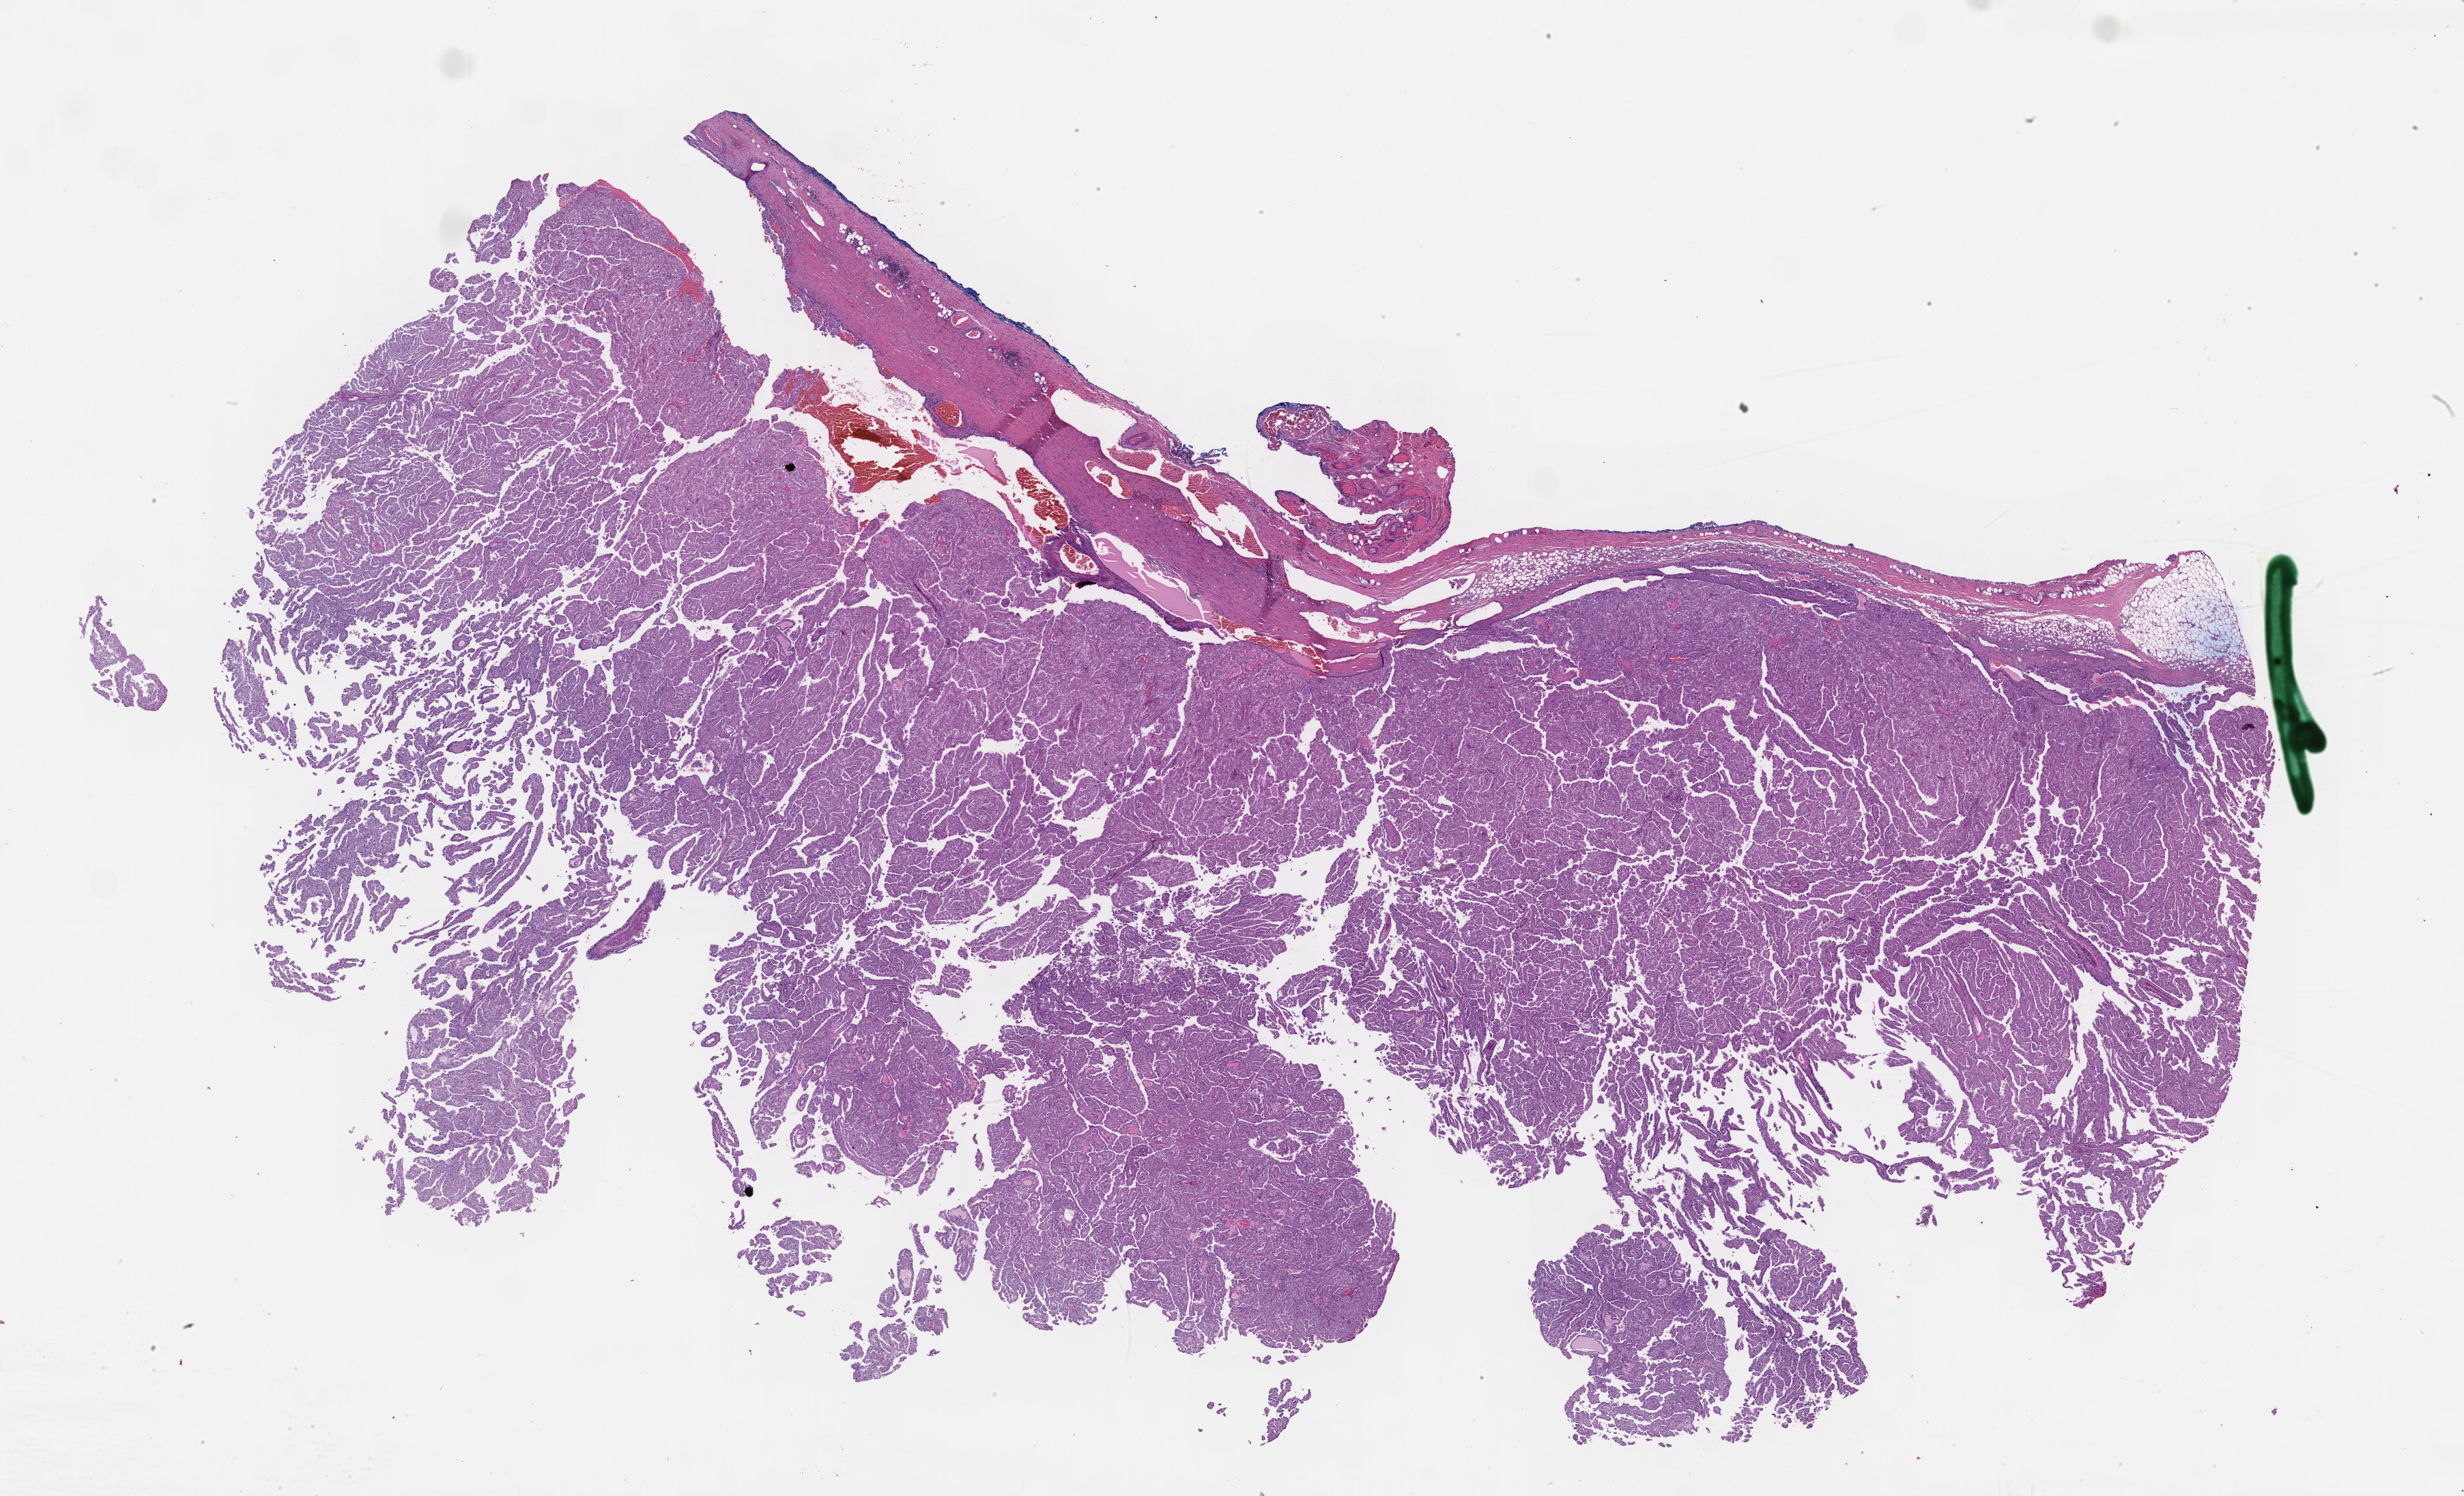
Whole-slide histology image, Hematoxylin and eosin (H&E) stained, whole scanned area (about 29.2 x 17.7 mm) shown as a low-resolution overview. FFPE section. Sample: primary tumour, kidney. Male patient; age at initial diagnosis 57 years.
AJCC pathologic stage: III (7th edition). Laterality: left. Diagnosis: Papillary adenocarcinoma, NOS. Lymph nodes positive (case pathology): 4 of 4 examined.